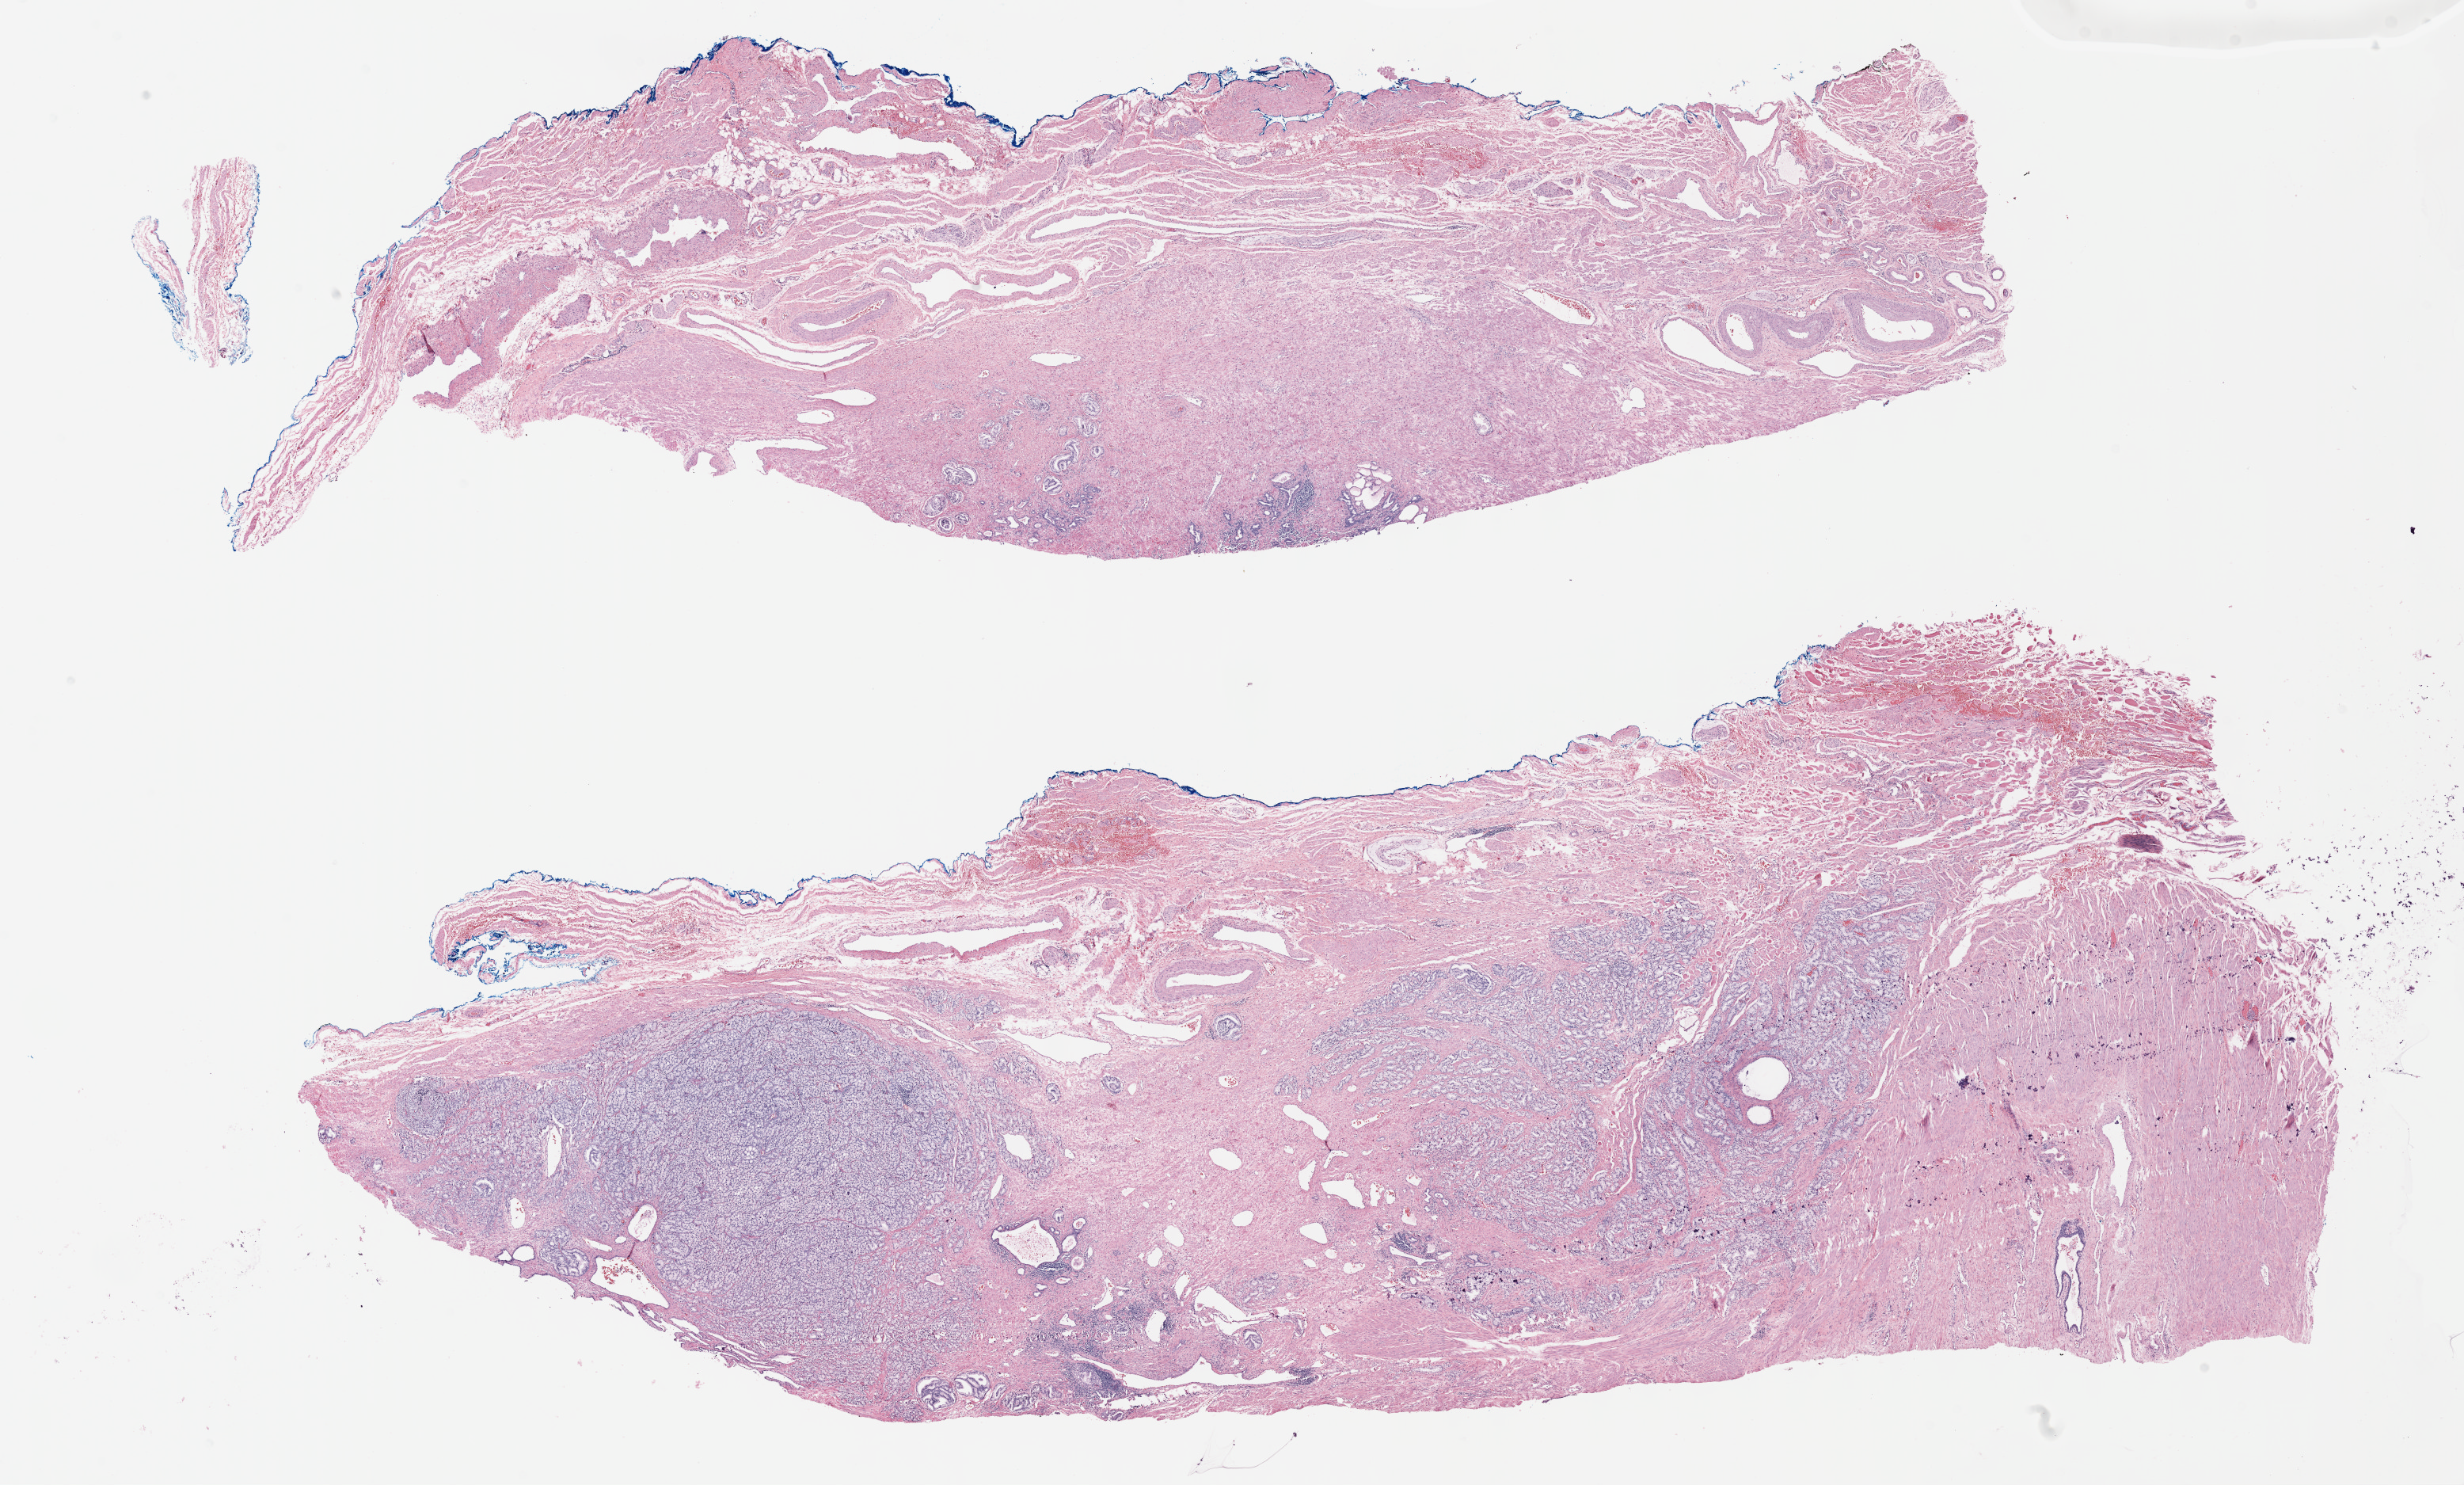
Digitized H&E-stained tissue section (whole slide), whole scanned area (about 25.2 x 15.2 mm, acquisition: 40x scan) shown as a low-resolution overview; FFPE section; primary tumour sample from the prostate. Patient: male, age at initial diagnosis 70 years. Gleason score: 8 (4+4).
Diagnosis: Adenocarcinoma, NOS (prostate gland). Laterality: bilateral. Lymph nodes positive (case pathology): 0 of 4 examined.